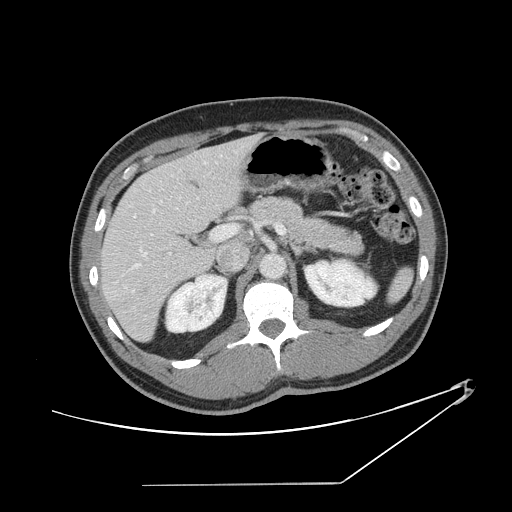
Contrast-enhanced abdominal CT, one axial slice. Position 80 of 152 along the scan axis. Intravenous contrast given. Soft-tissue window (W 400 / L 40 HU). 512 × 512 image matrix, field of view 432 × 432 mm. Male patient, age 45 years. Case-level facts recorded for this patient, not image findings: diagnosis: colorectal cancer liver metastases, imaged before liver resection; multiple liver metastases: no; largest metastasis: 1 cm; disease in both lobes: no.
Structures marked on this image (expert manual segmentation):
- hepatic veins: box from (x=111, y=155) to (x=222, y=292) px
- liver: (x=102, y=137)–(x=256, y=340)
- planned liver remnant (the part of the liver to remain after resection): (x=102, y=156)–(x=215, y=340)
- portal vein (with intrahepatic branches): (x=134, y=224)–(x=285, y=268)